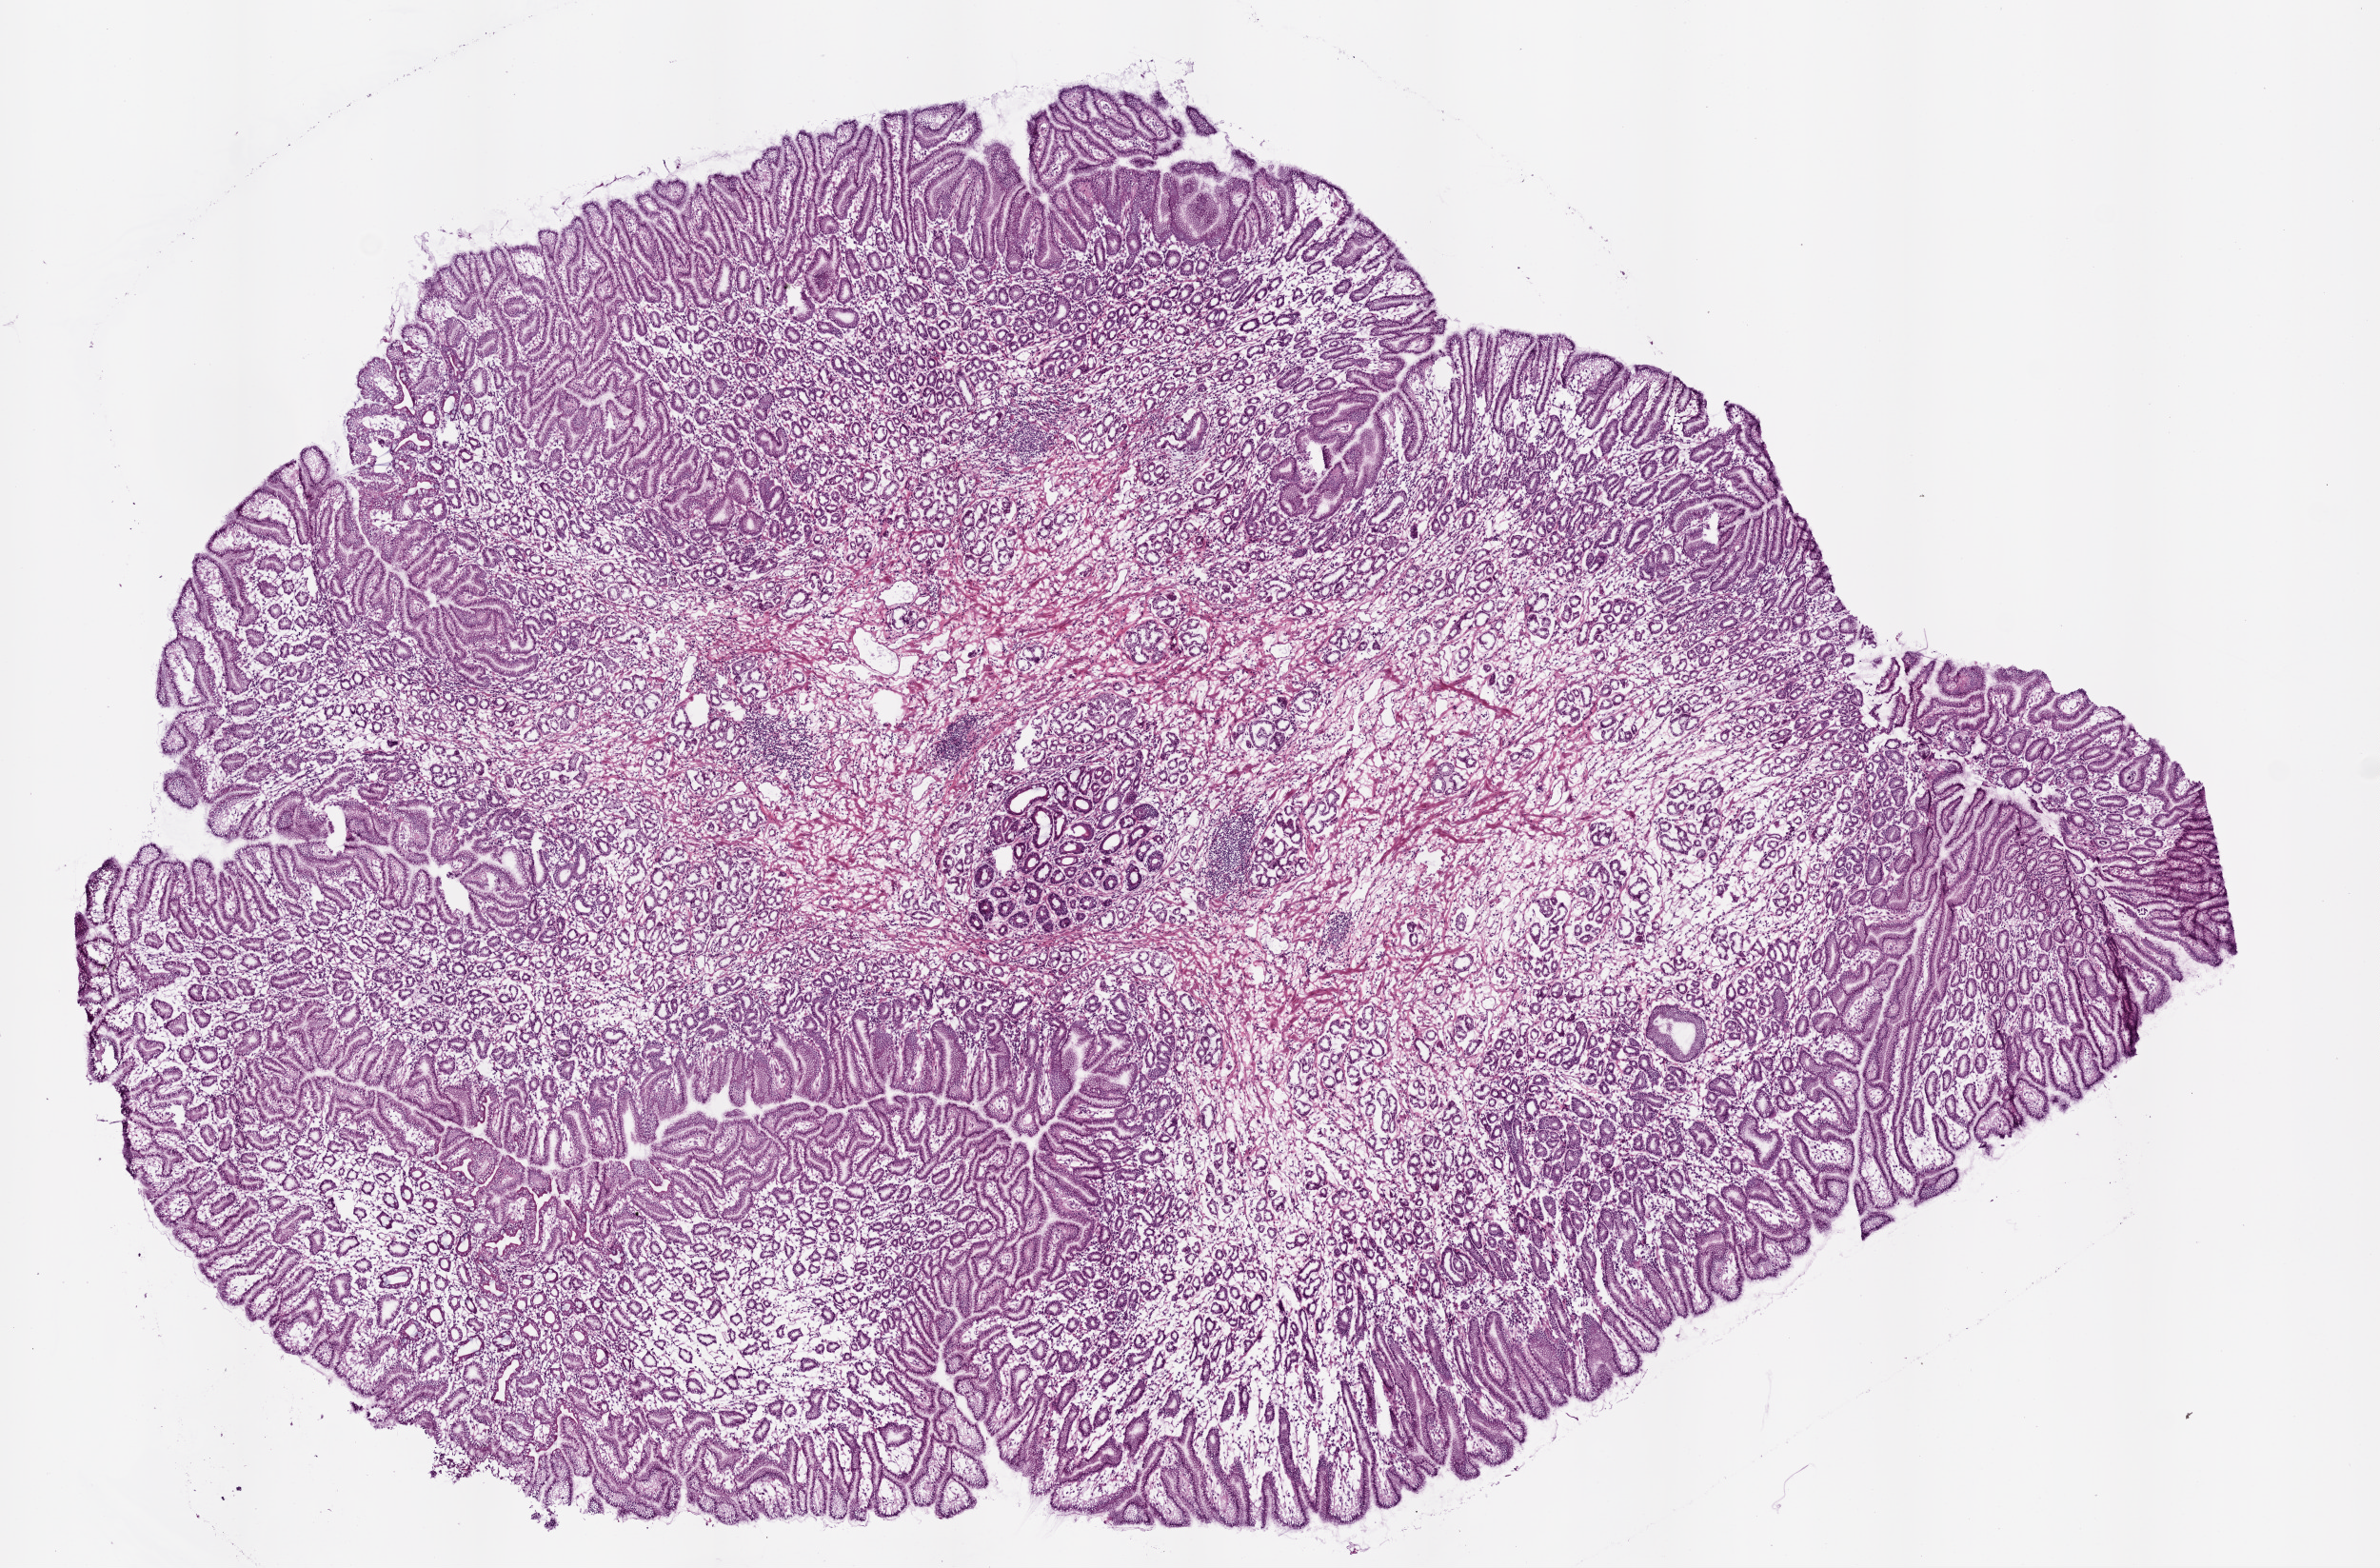
Whole-slide histology image, H&E-stained — low-resolution overview of the scanned area, about 10.0 x 6.6 mm (from a 20x scan); frozen section from the top of the tissue portion; solid tissue normal (non-tumour tissue) sample from the stomach. Male, age 66 years at initial diagnosis.
• this section: solid tissue normal (non-tumour) sample from the same patient
• patient diagnosis: Adenocarcinoma, intestinal type (cardia, NOS)